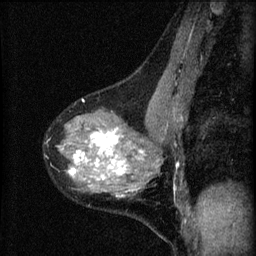
Breast MRI (dynamic contrast-enhanced), one sagittal slice; position 35 of 60 along the scan axis; dynamic contrast-enhanced series, image 2 of 4 at this slice position (ordered by acquisition); 1.5 T; TE 4.2 ms, TR 8.2 ms; 2 mm slice thickness; 256 × 256 image matrix, field of view 180 × 180 mm. Female patient, age 41 years.
Outlined on this slice (semi-automatic segmentation, software-assisted and operator-edited):
- analysis volume of interest (the breast-tissue region the enhancement analysis was run in; not a lesion): box from (x=45, y=91) to (x=166, y=198) px
- tumour enhancement mask (voxels above the 70 % enhancement threshold inside the analysis volume of interest): (x=68, y=129)–(x=146, y=196)